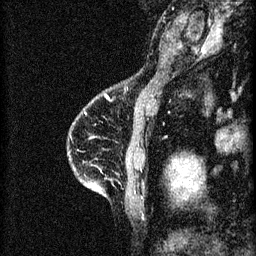
Breast MRI (dynamic contrast-enhanced), one sagittal slice. Position 19 of 60 along the scan axis. 3 images stored at this slice position (order not interpretable as contrast timing). 1.5 T. TE 4.2 ms, TR 8.2 ms. 2 mm slice thickness. 256 × 256 image matrix, field of view 180 × 180 mm. Patient: female, 46 years.
Annotated regions visible in this slice (semi-automatically segmented with operator editing):
- analysis volume of interest (the breast-tissue region the enhancement analysis was run in; not a lesion): box from (x=68, y=114) to (x=148, y=209) px
- tumour enhancement mask (voxels above the 70 % enhancement threshold inside the analysis volume of interest): (x=91, y=184)–(x=93, y=187)